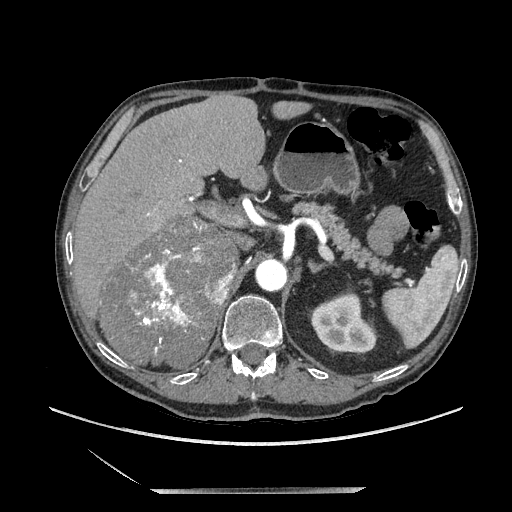
Contrast-enhanced abdominal CT, one axial slice; slice 136 of 243 in the series (ordered by position); soft-tissue window (W 400 / L 40 HU); 512 × 512 image matrix, field of view 420 × 420 mm. Male patient. From the clinical record (not read from this slice): diagnosis: adrenocortical carcinoma; tumour side: right adrenal; tumour size at pathology: 16 cm; Ki-67 index: 17 %; stage (as recorded): 3.
Annotated regions visible in this slice (semi-automatically segmented with operator editing):
- mass: bounding box [x1, y1, x2, y2] px = [104, 221, 236, 367]